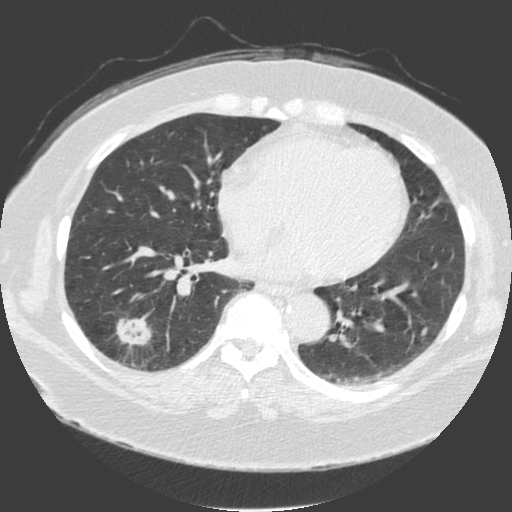
Low-dose screening chest CT, axial slice; third screening round (two years after baseline); lung window (W 1500 / L -600 HU); 2 mm slice thickness; slice 100 of 175 in the series. Female participant, aged 56 years at enrolment. Current smoker at enrolment.
Expert-annotated lung lesion, bounding box [x1, y1, x2, y2] px = [104, 303, 157, 354]. The screening reader recorded 4 non-calcified nodules or masses ≥4 mm on this exam; which of them this box marks is not recorded. Official screen result: positive, other. Later outcome: lung cancer diagnosed 20 days after this screen — adenosquamous carcinoma, right lower lobe, poorly differentiated (G3), stage IA (AJCC 6th edition), 25 mm at pathology.